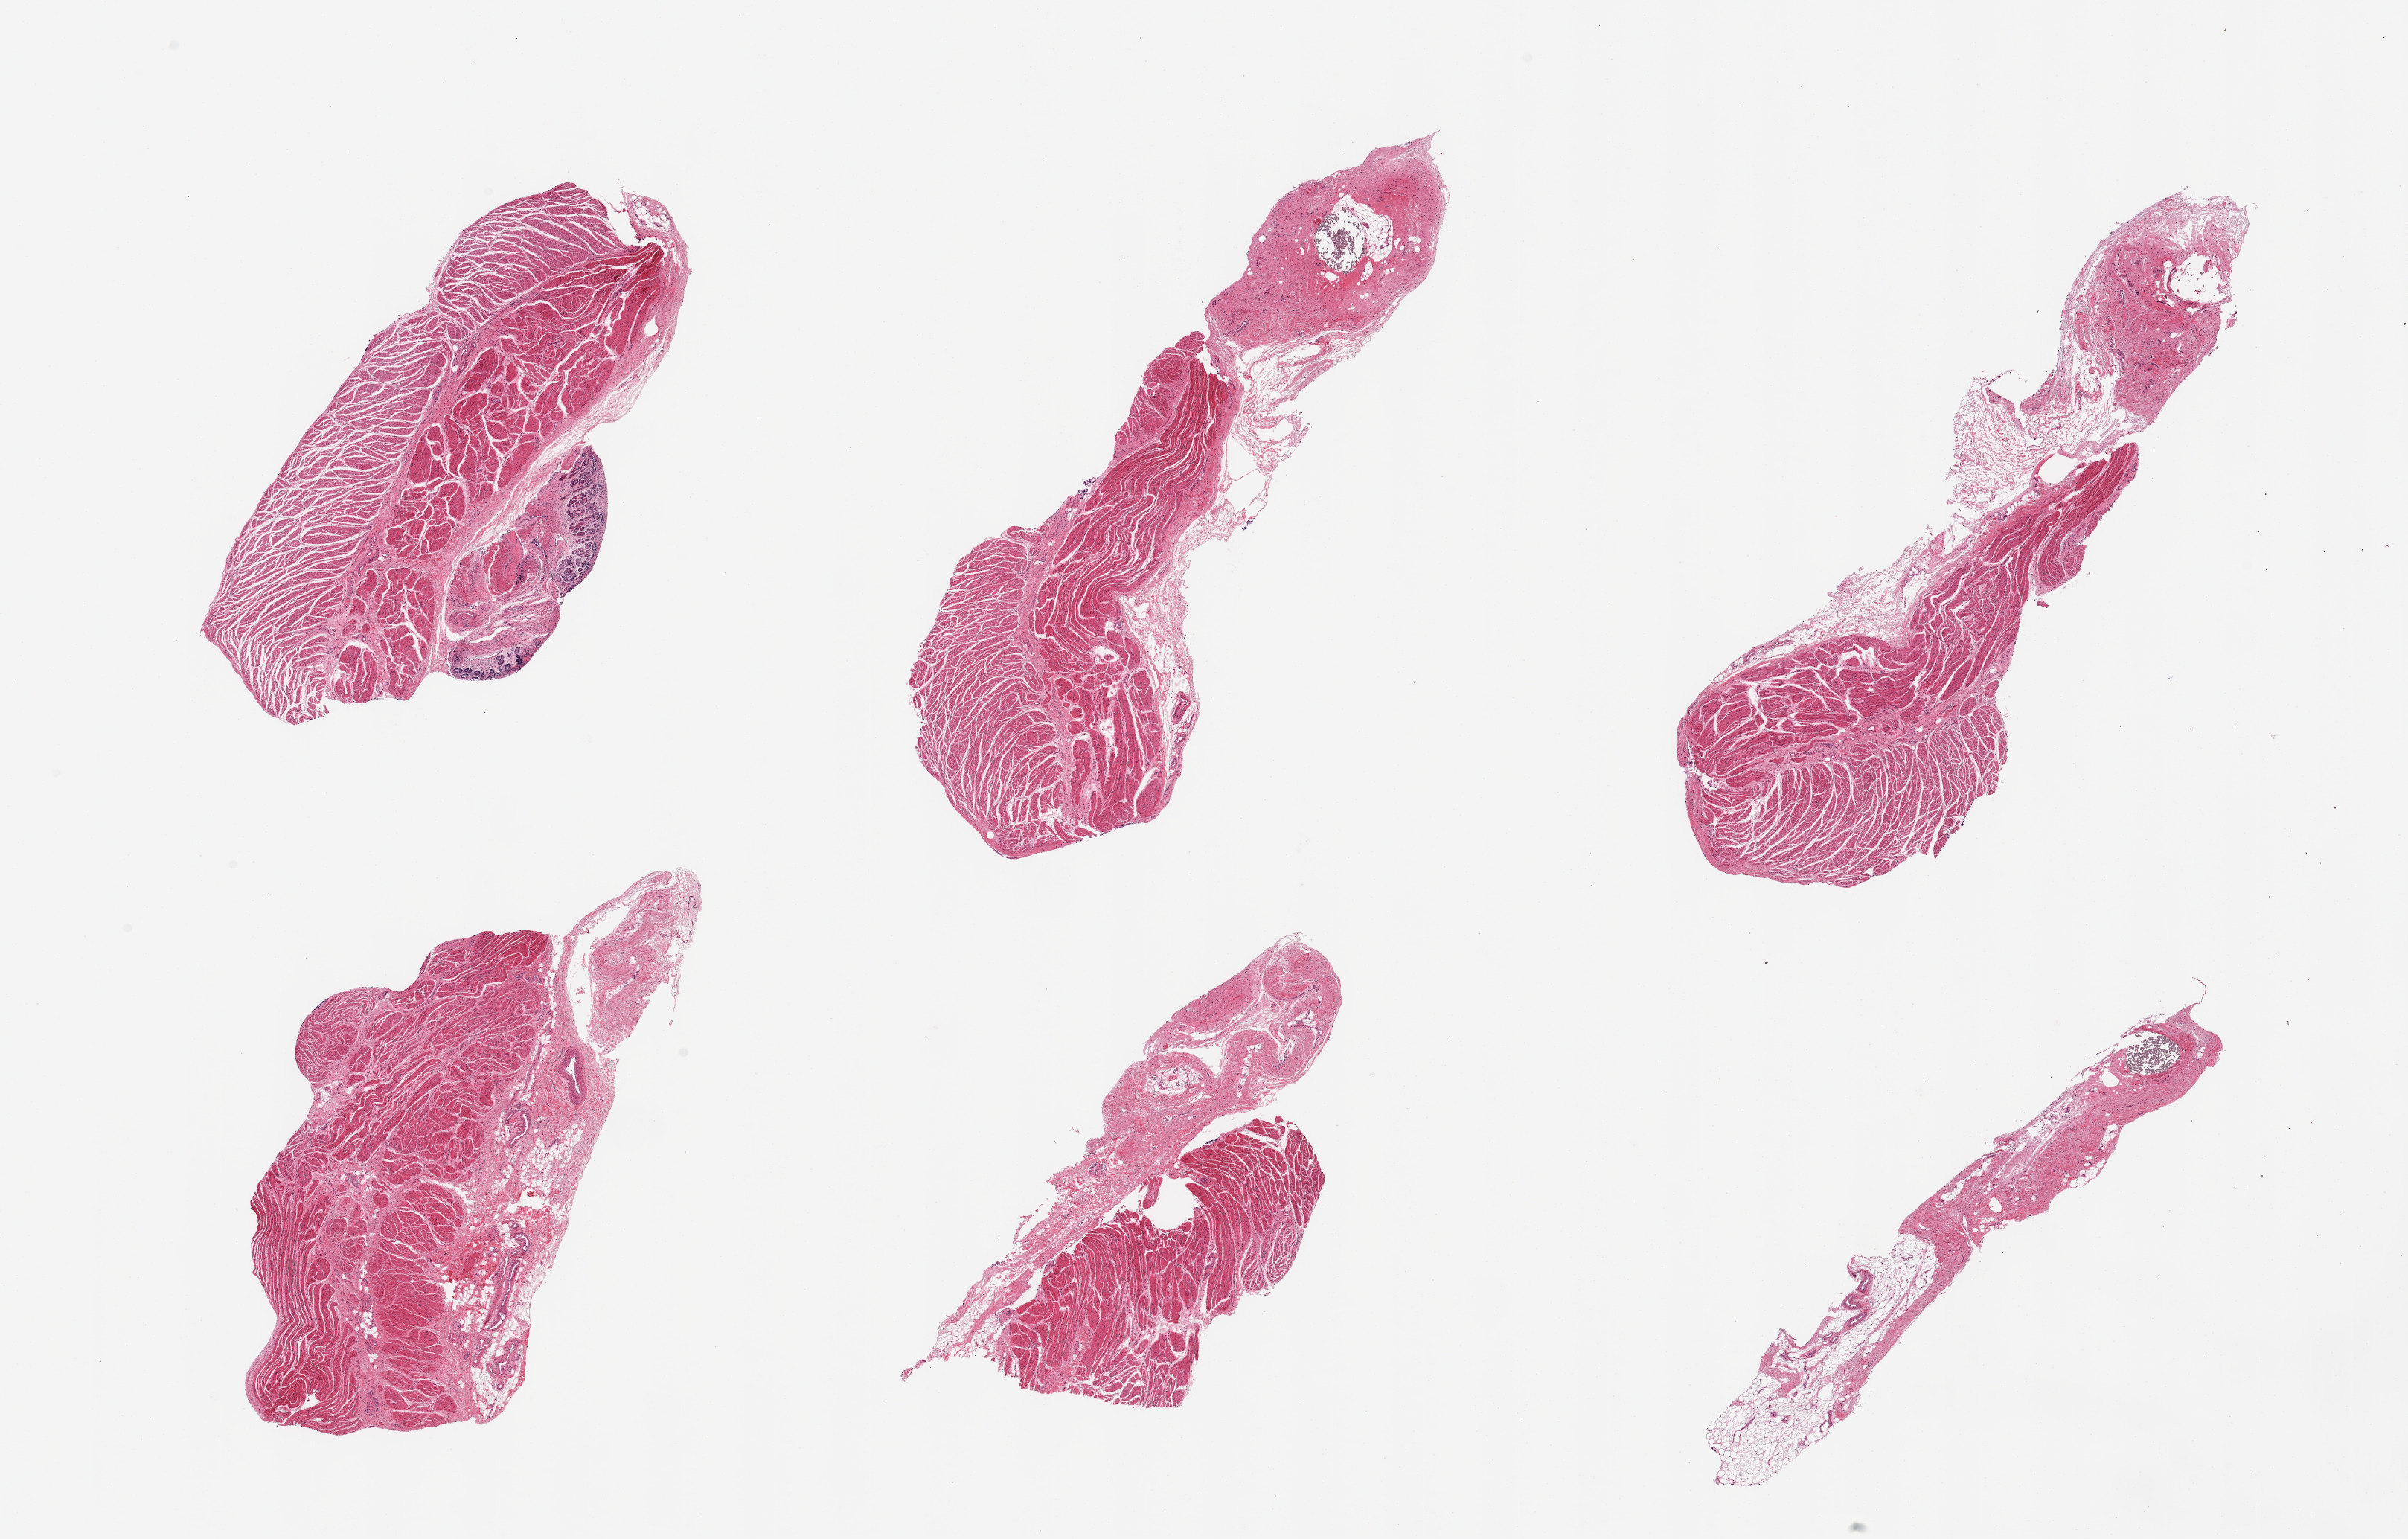
Digitized hematoxylin and eosin (H&E)-stained section, brightfield — shown as a low-resolution overview of the whole scanned area (about 25.6 x 16.4 mm, slide scanned at 20x), PAXgene-fixed paraffin-embedded (PFPE) section, target tissue: gastroesophageal junction, tissue donor sample.
Pathologist's review note for this sample: 6 pieces; target muscularis with residual attached mucosa in one piece, and attached fibrovascular and fatty tissue with suture material.